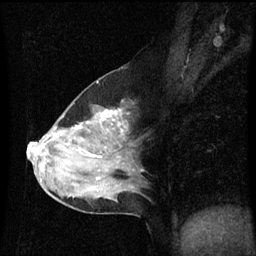
Breast MRI (dynamic contrast-enhanced), one sagittal slice; dynamic contrast-enhanced series, image 2 of 3 at this slice position (ordered by acquisition); 1.5 T; TE 4.2 ms, TR 8.9 ms; 2 mm slice thickness; 256 × 256 image matrix. Patient: female, 50 years. Case-level facts recorded for this patient, not image findings: setting: breast cancer imaged before/during neoadjuvant chemotherapy; receptor status: HR-positive, HER2-negative.
Structures marked on this image (semi-automatic segmentation, software-assisted and operator-edited):
- analysis volume of interest (the breast-tissue region the enhancement analysis was run in; not a lesion): bounding box <33,90,138,209> (left, top, right, bottom; pixels)
- tumour enhancement mask (voxels above the 70 % enhancement threshold inside the analysis volume of interest): <33,110,119,145>